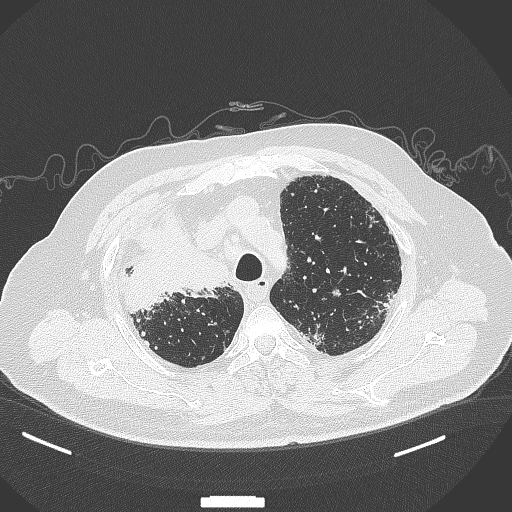
Chest CT, one axial slice. Slice 285 of 384 in the series (ordered by position). Reconstruction kernel B70f. Lung window (W 1500 / L -600 HU). 1 mm slice thickness. 512 × 512 image matrix, field of view 400 × 400 mm. Male patient, age 69 years. Case-level facts recorded for this patient, not image findings: clinical TNM (as recorded): T4 N3 M1.
Annotated regions visible in this slice (bounding box drawn by a radiologist):
- lung tumour (recorded histology: adenocarcinoma): bounding box [x1, y1, x2, y2] px = [121, 212, 230, 311]